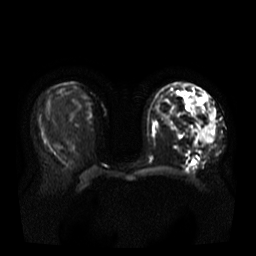
Breast MRI, one axial slice. Position 19 of 37 along the scan axis. Diffusion-weighted series; image 2 of 4 stored at this slice position (different b-values; order by instance number). 3 T. 5 mm slice thickness. 256 × 256 image matrix. Female patient.
Annotated regions visible in this slice (manually delineated by an expert):
- tumour on diffusion-weighted imaging: bounding box (x1, y1, x2, y2) in pixels: (199, 107, 215, 143)